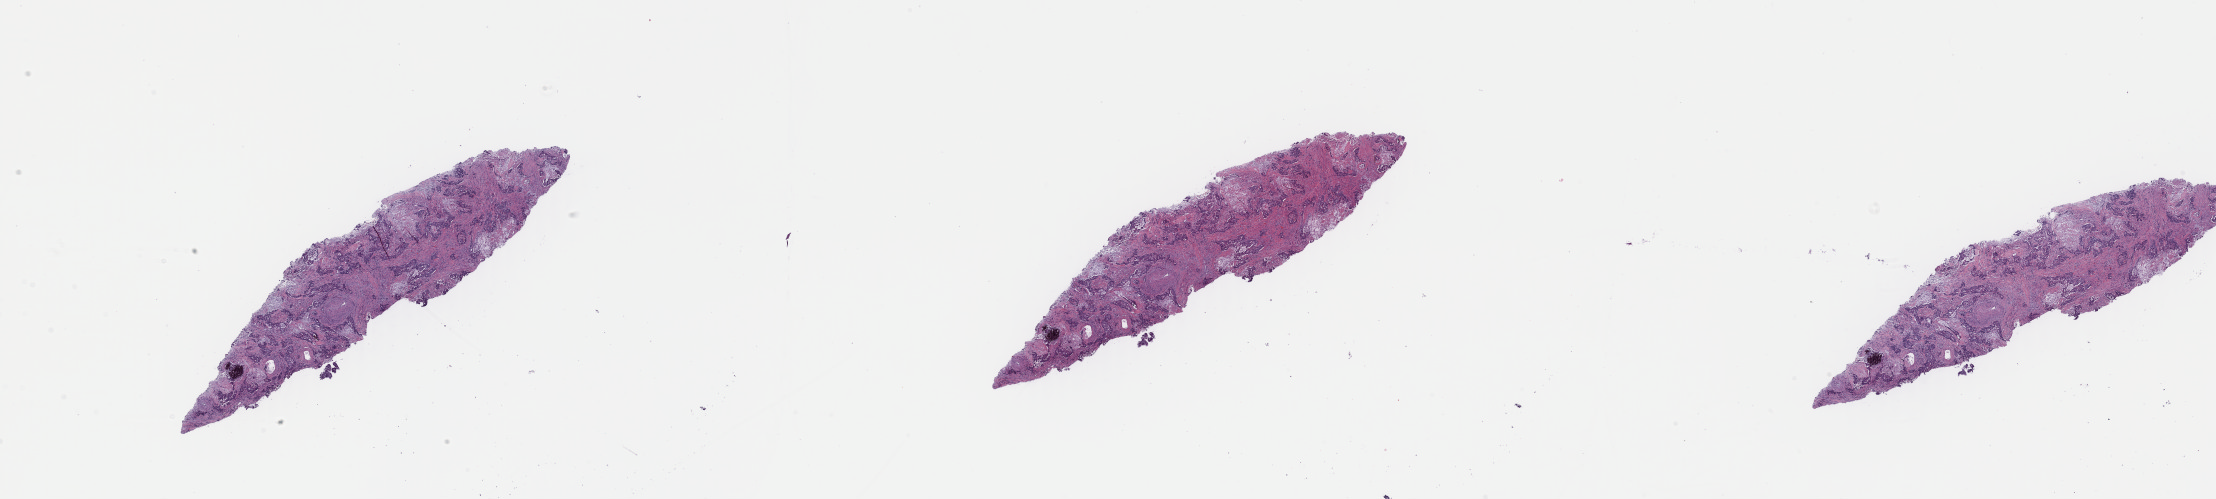
Whole-slide histology image, H&E-stained, shown as a low-resolution overview of the whole scanned area (about 35.0 x 7.9 mm). Formalin-fixed paraffin-embedded (FFPE) diagnostic section. Primary tumour sample from the rectum. Patient: male, age at initial diagnosis 39 years.
Diagnosis: Adenocarcinoma, NOS (rectosigmoid junction).